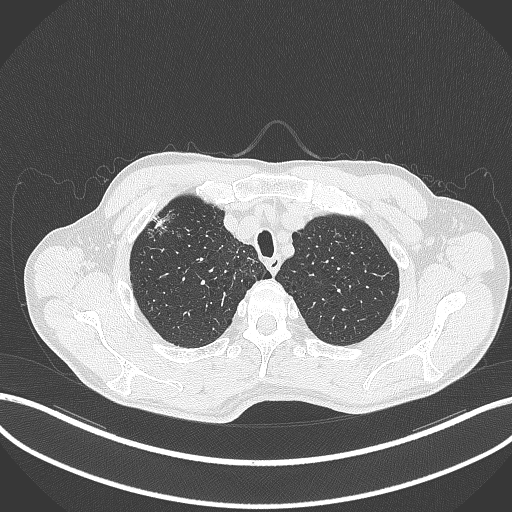
Chest CT, one axial slice; position 361 of 427 along the scan axis; lung window (W 1500 / L -600 HU); 1 mm slice thickness; 512 × 512 image matrix, field of view 400 × 400 mm. Patient: male, 69 years. From the clinical record (not read from this slice): clinical TNM (as recorded): T1b N1 M0.
Outlined on this slice (rectangle marked by the reading radiologist):
- lung tumour (recorded histology: adenocarcinoma): bounding box <148,211,169,232> (left, top, right, bottom; pixels)